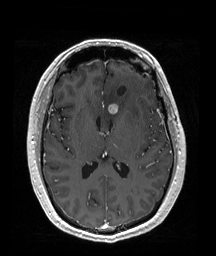
Brain MRI from a brain-tumour surgery series, one axial slice; slice 91 of 192 in the series (ordered by position); T1-weighted post-contrast; 216 × 256 image matrix, field of view 211 × 250 mm. From the clinical record (not read from this slice): histopathology: Oligodendroglioma; WHO grade: 2; IDH mutation: yes; tumour location: Left Frontal (septal).
Outlined on this slice (manually delineated by an expert):
- tumour: bounding box (x1, y1, x2, y2) in pixels: (107, 103, 132, 114)